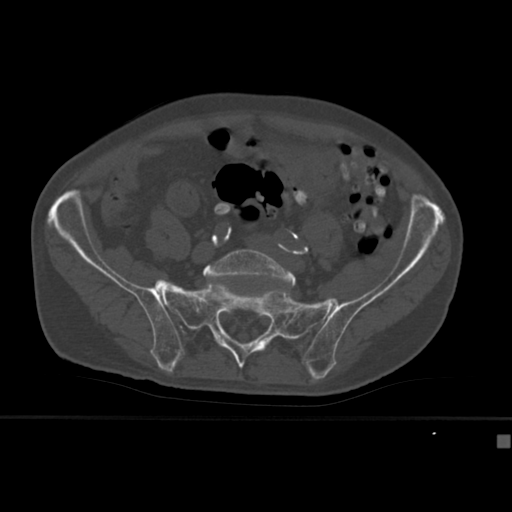
CT including the spine, one axial slice. Position 73 of 430 along the scan axis. 120 kVp. Bone window (W 1800 / L 400 HU). 512 × 512 image matrix, field of view 337 × 337 mm. Male patient, age 64 years. From the clinical record (not read from this slice): primary cancer: uterus.
Annotated regions visible in this slice (semi-automatically segmented with operator editing):
- L5 vertebra: bounding box <203,249,296,288> (left, top, right, bottom; pixels)